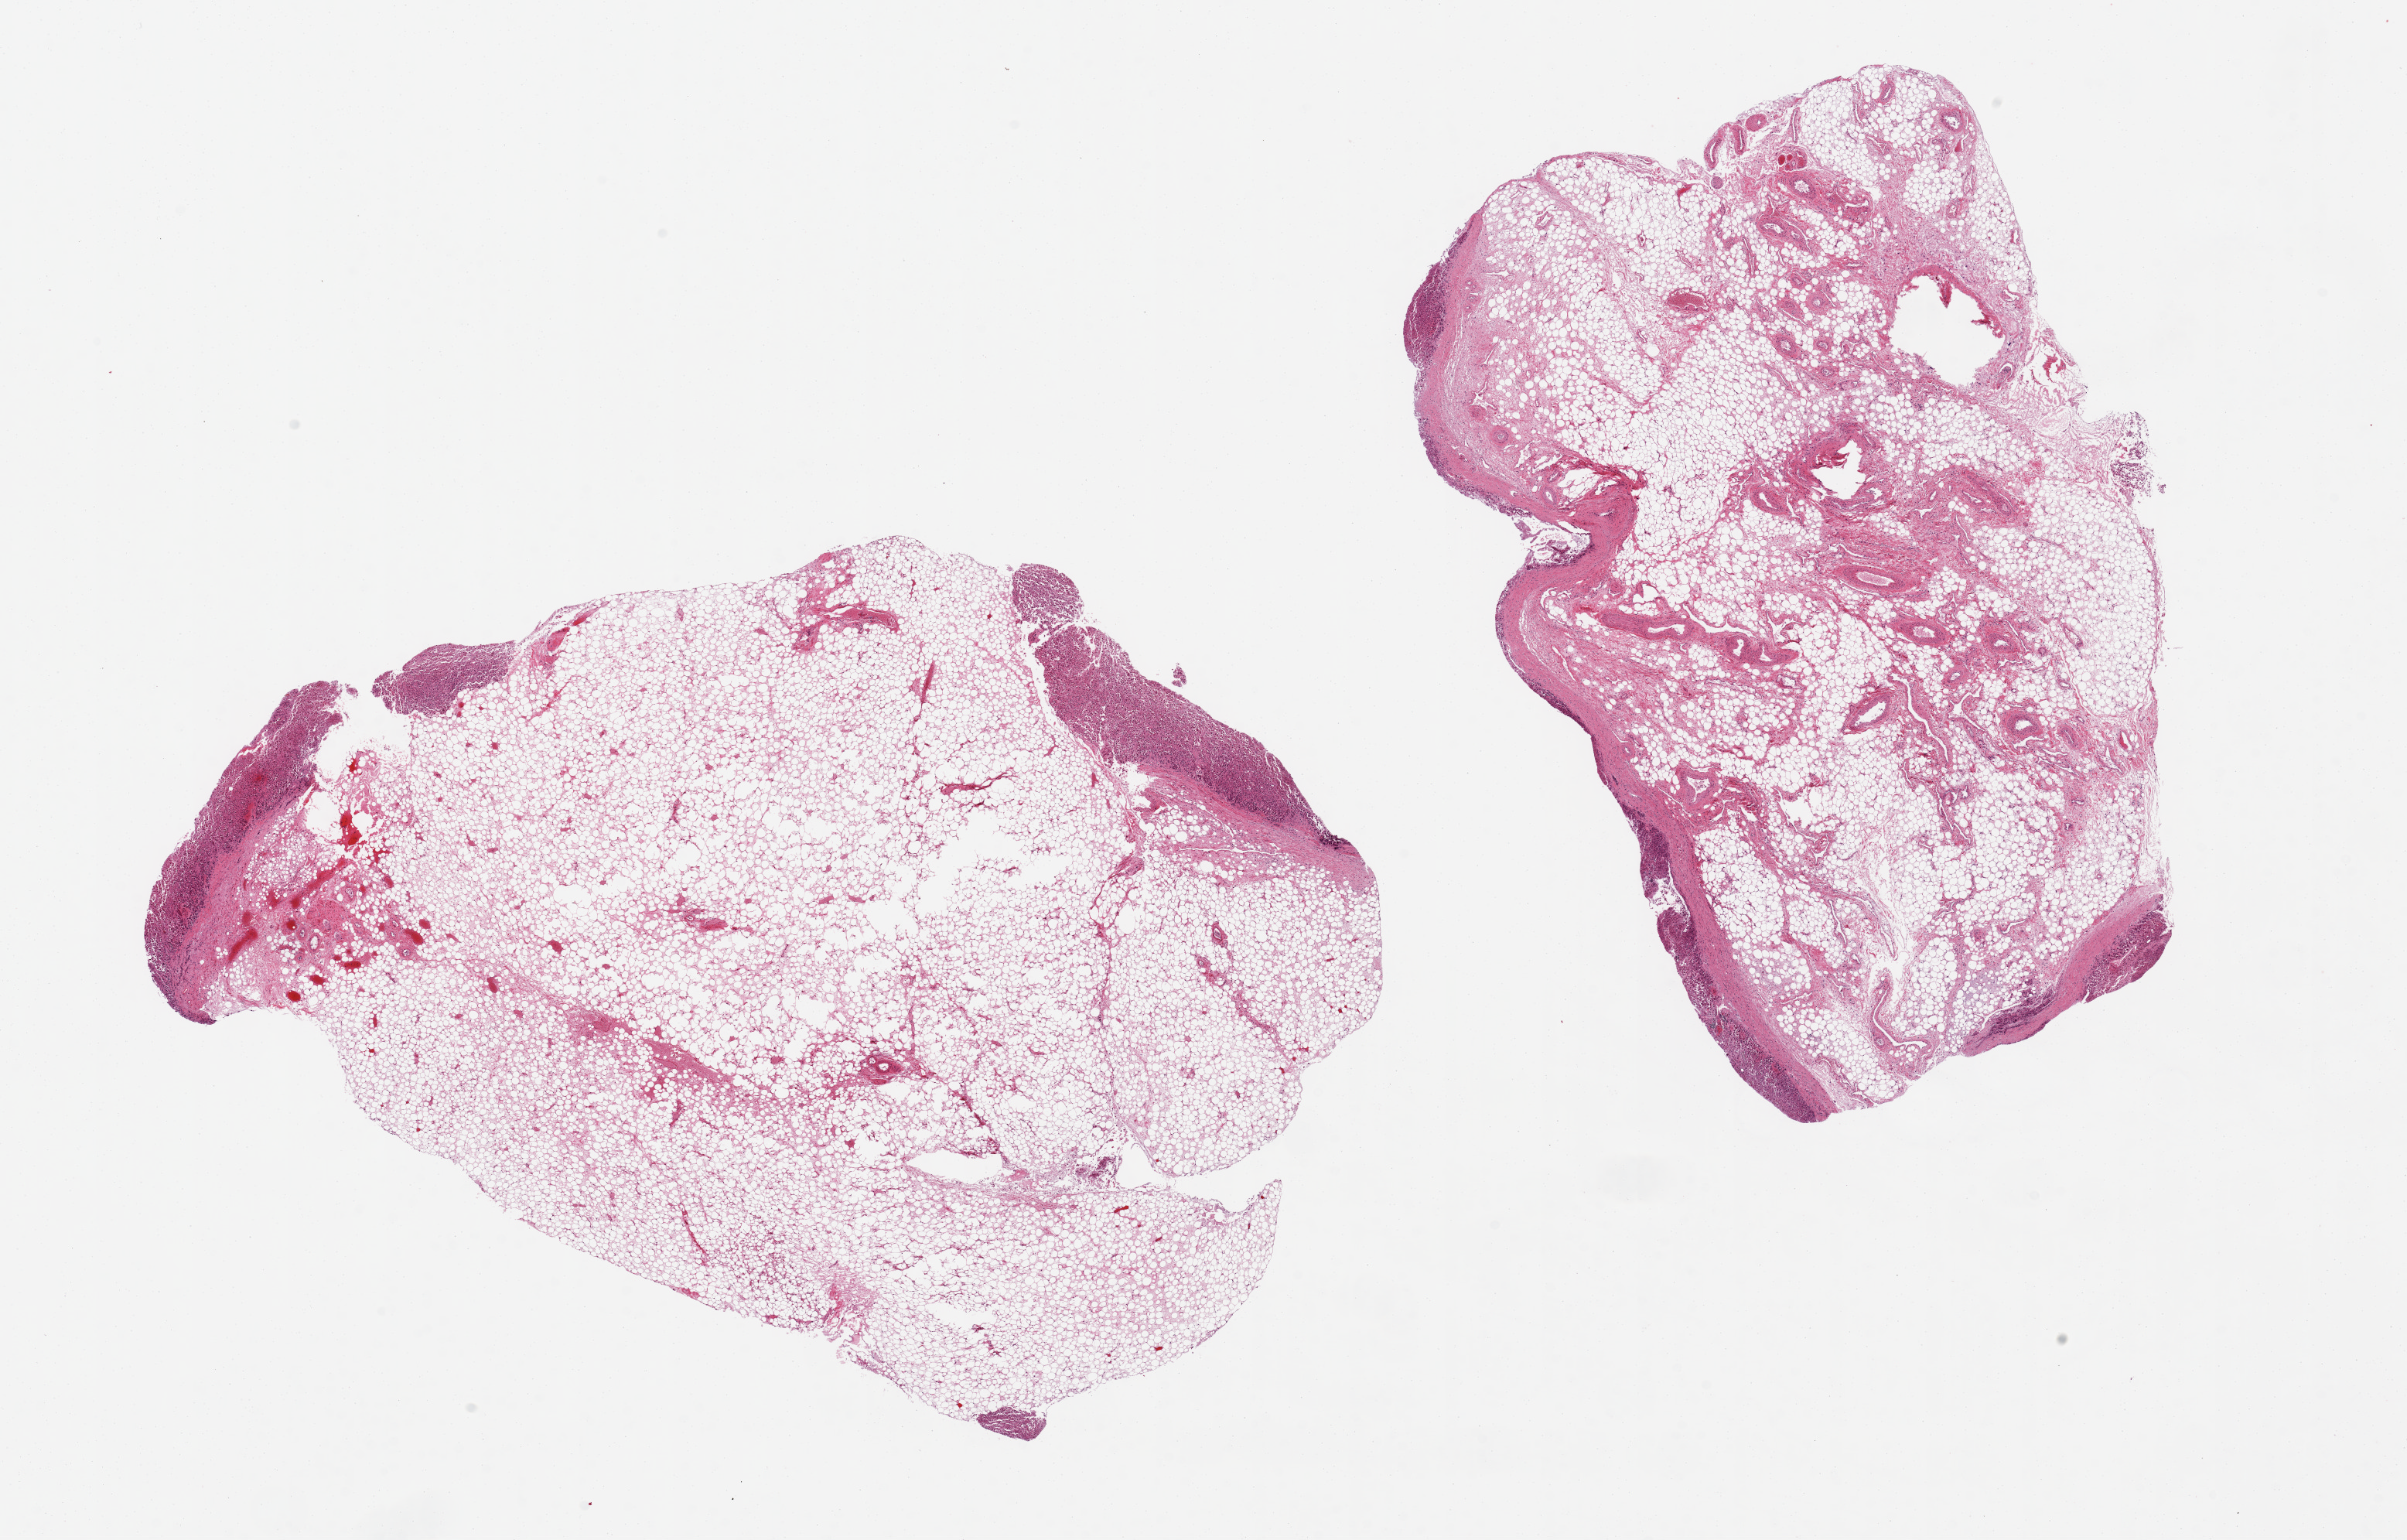
Digitized H&E-stained section, brightfield — shown as a low-resolution overview of the whole scanned area (about 24.6 x 15.7 mm, slide scanned at 20x), PAXgene-fixed, paraffin-embedded tissue, target tissue: adrenal gland, donor tissue sample. Donor: female.
- reviewer comment on this tissue sample: 2 pieces 11x9 & 10x4 mm; >90% adipose, only a thin rim of adrenal (autolyzed) present